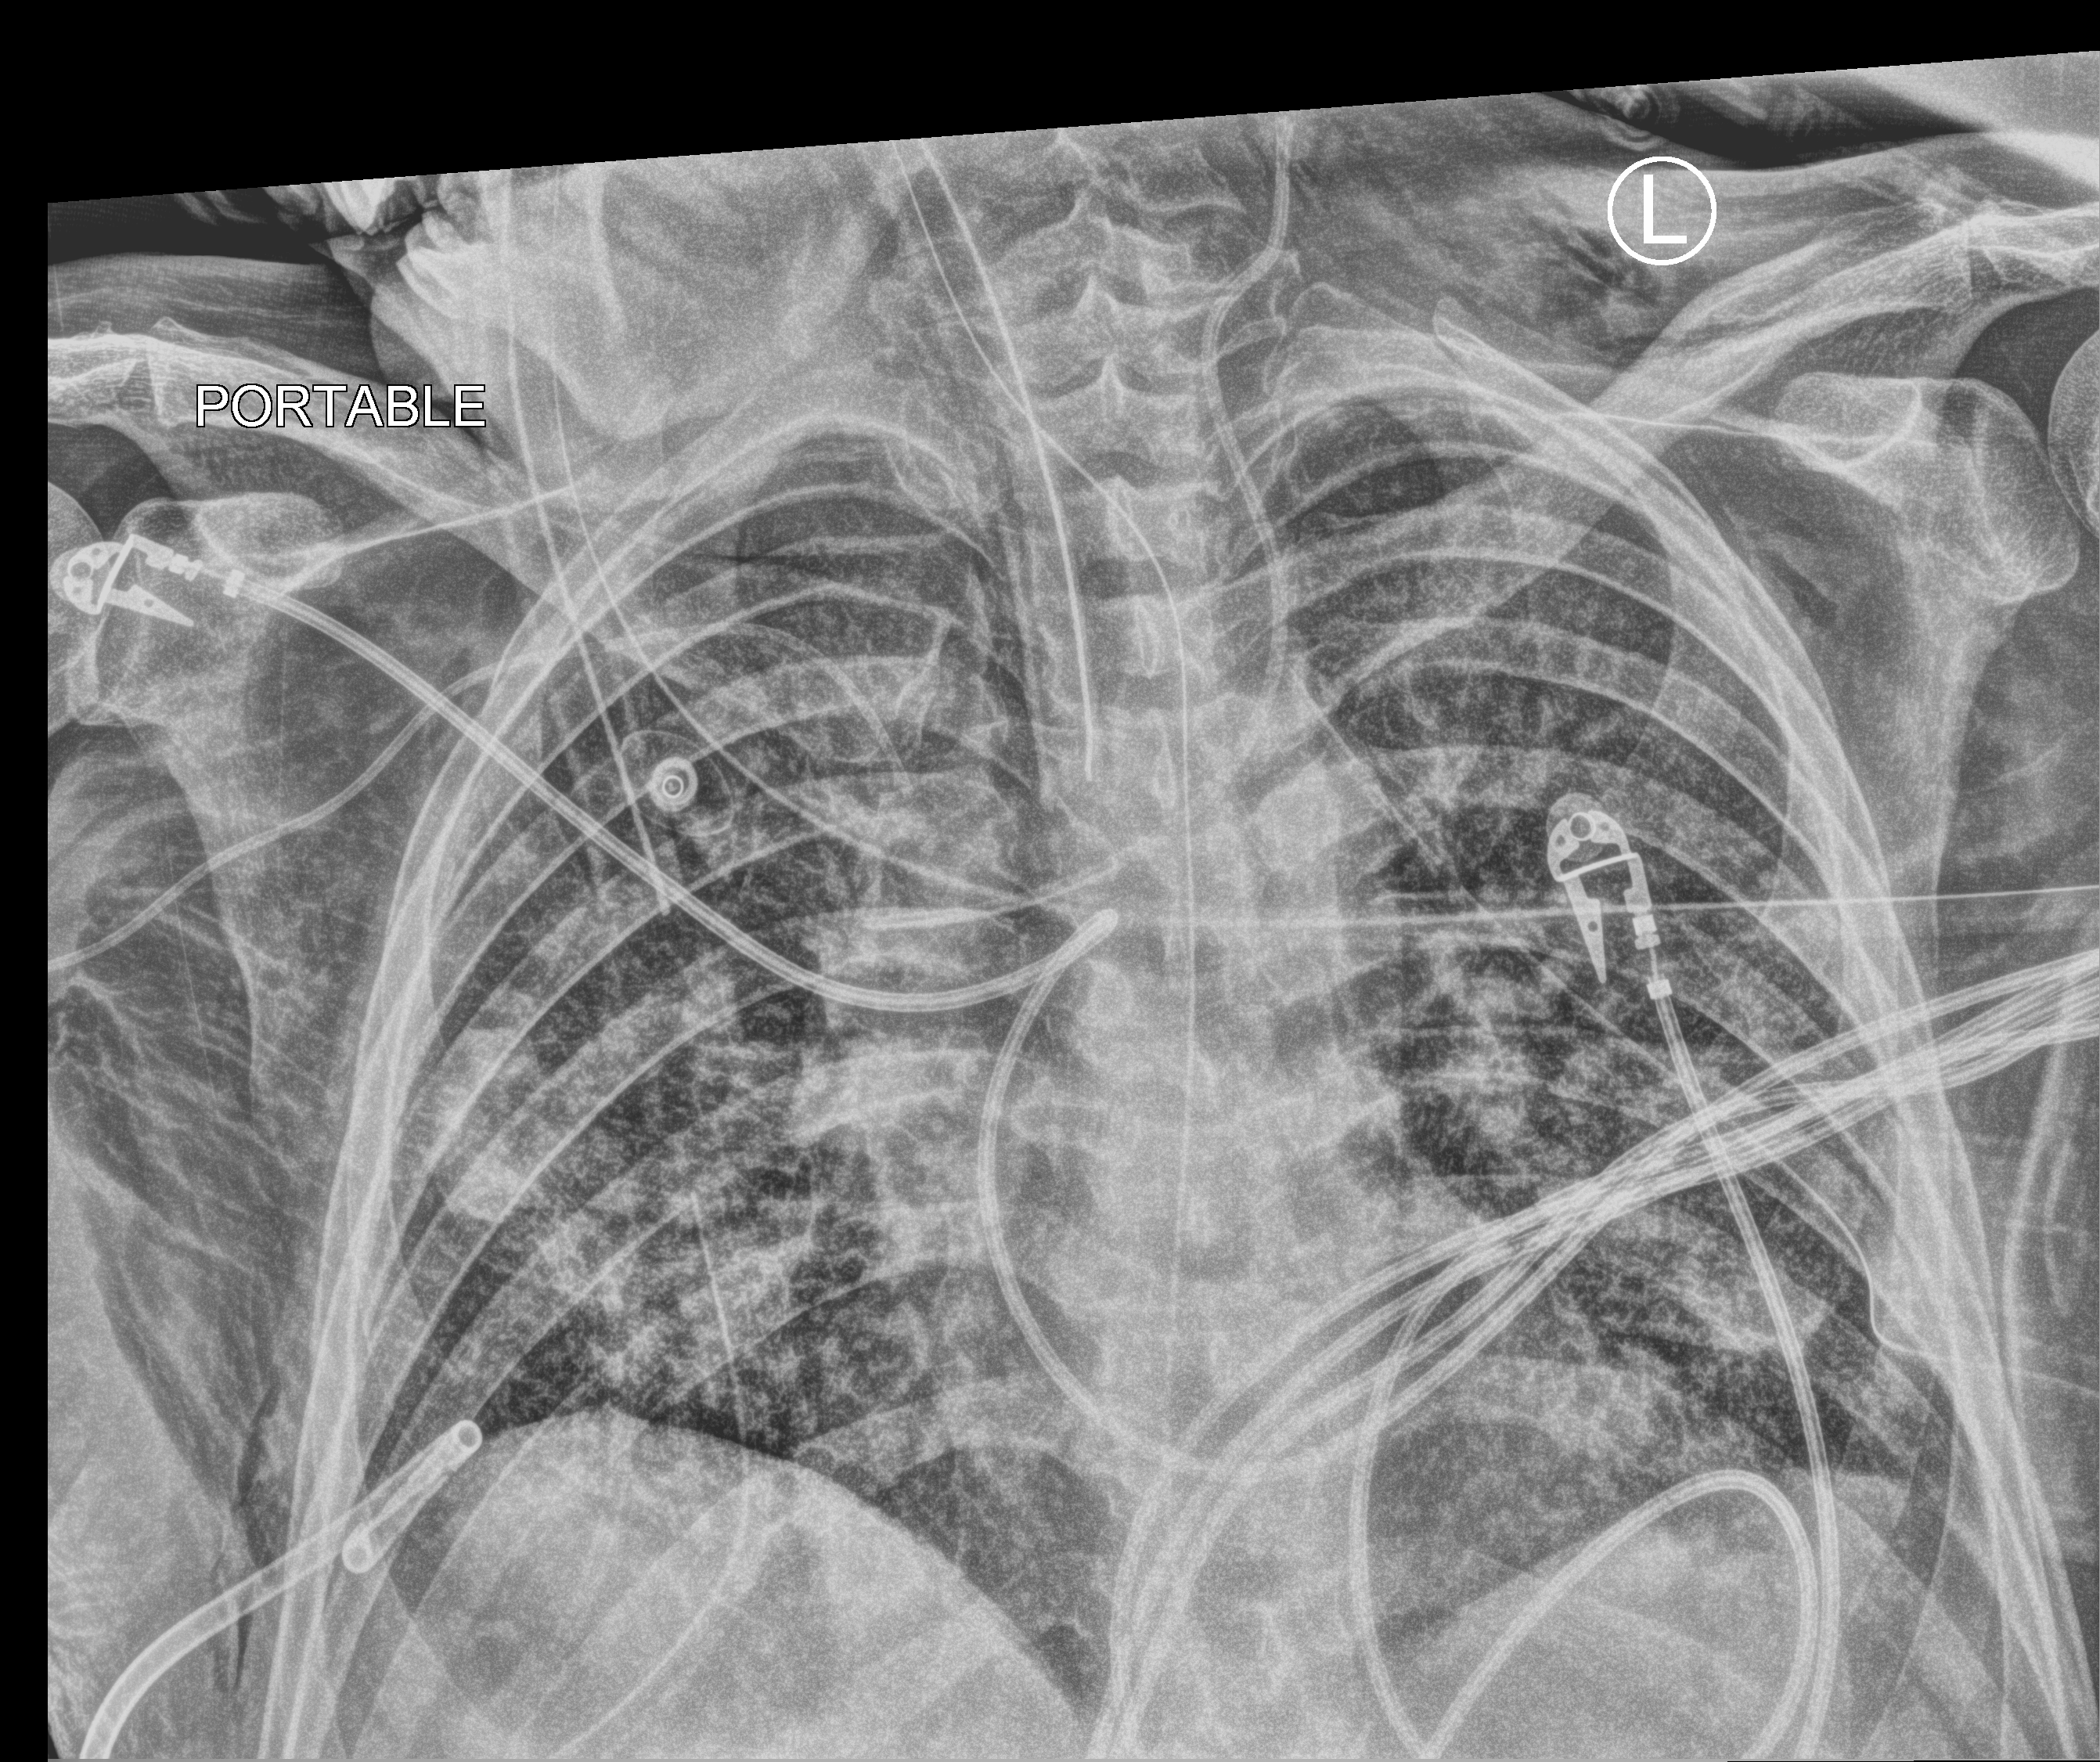
Portable chest radiograph. Patient hospitalised with COVID-19; male, aged 18–59 years.
From the hospital-stay record, not from the radiograph (when in the stay this image was taken is not recorded): length of hospital stay: 77 days; COPD (admission record): no.